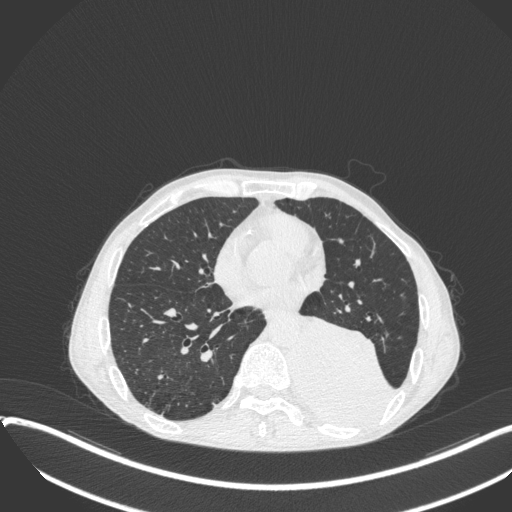
Chest CT, one axial slice; position 147 of 400 along the scan axis; 120 kVp; lung window (W 1500 / L -600 HU); 512 × 512 image matrix, field of view 400 × 400 mm. Male patient, age 57 years. Case-level facts recorded for this patient, not image findings: clinical TNM (as recorded): T4 N0 M0.
Outlined on this slice (rectangle marked by the reading radiologist):
- lung tumour (recorded histology: squamous cell carcinoma): bounding box [x1, y1, x2, y2] px = [283, 307, 394, 434]